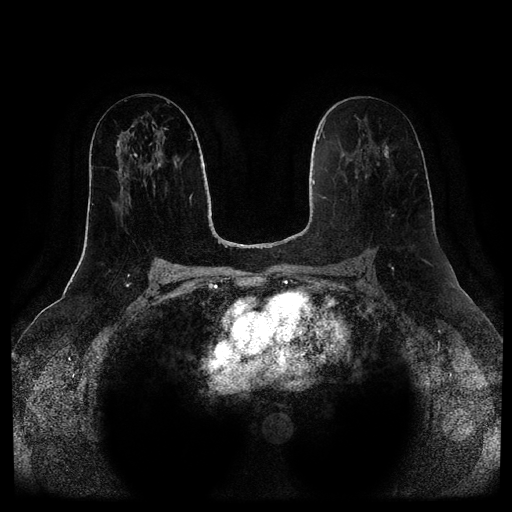
Breast MRI (dynamic contrast-enhanced, multi-phase), one axial slice. Slice 47 of 116 in the series (ordered by position). Dynamic contrast-enhanced series, time point 2 of 5 at this slice position (early post-contrast). 1.5 T. TE 2.6 ms, TR 5.2 ms. 2 mm slice thickness. 512 × 512 image matrix, field of view 380 × 380 mm. Patient: female, 57 years.
Annotated regions visible in this slice (semi-automatically segmented with operator editing):
- breast lesion (labelled benign in the annotation): box from (x=384, y=145) to (x=388, y=157) px